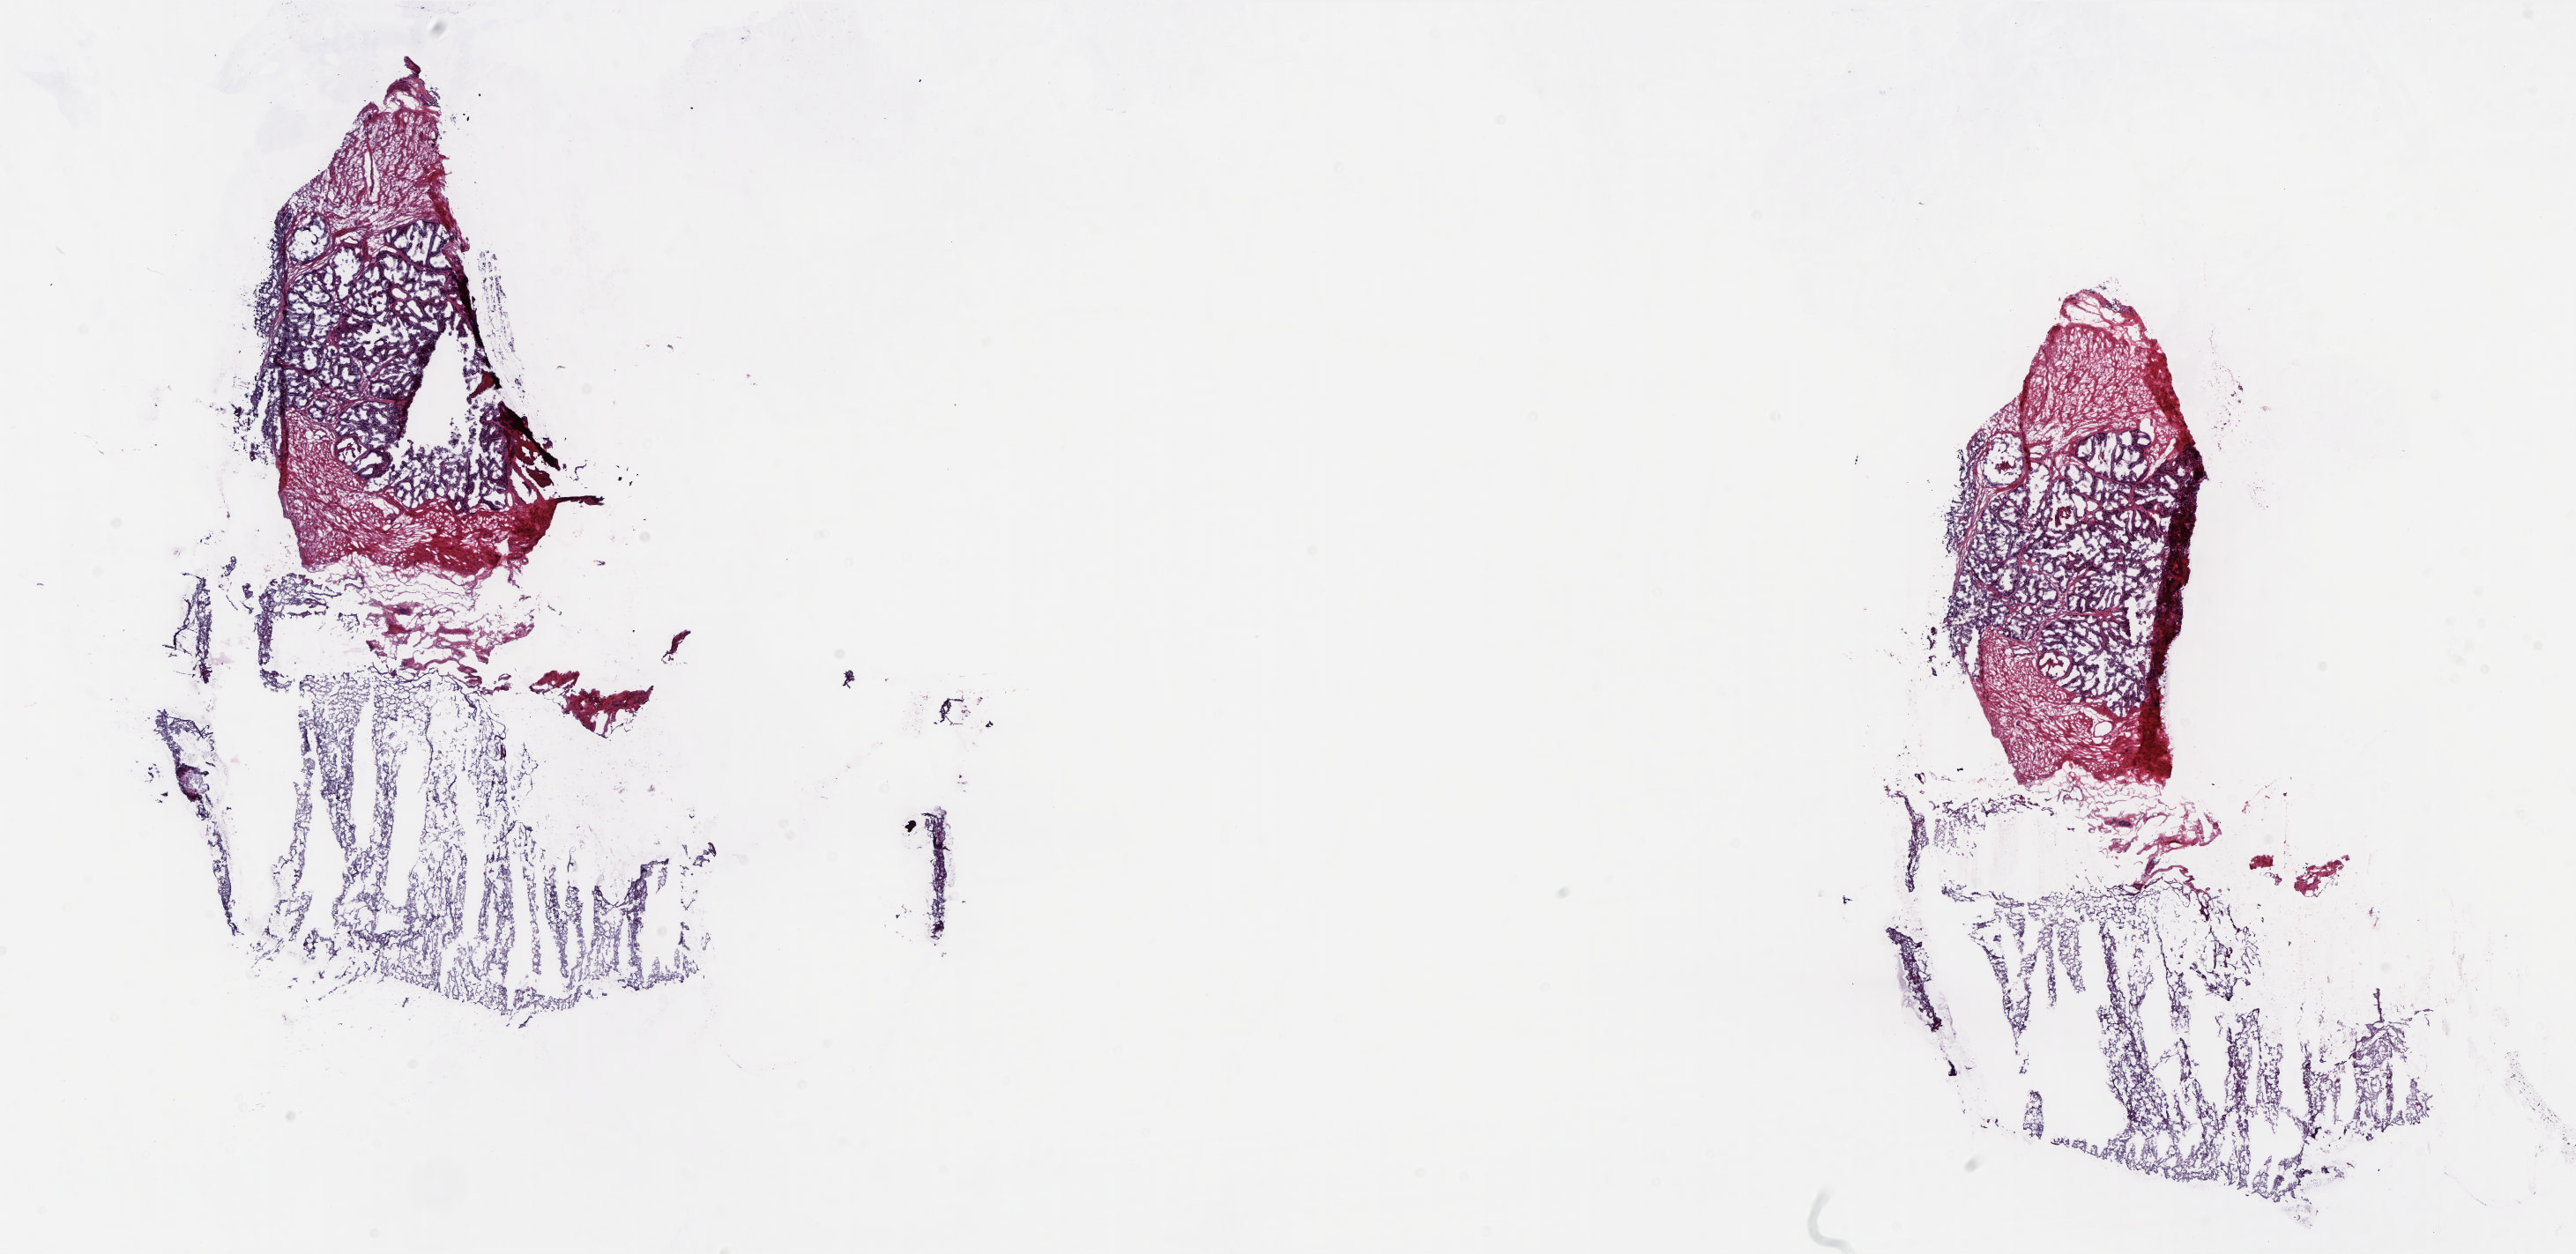
Digitized H&E tissue section (whole slide) — a low-resolution overview of the entire scanned area, about 23.6 x 11.5 mm (slide scanned at 20x). Frozen section from the top of the tissue portion. Prostate, solid tissue normal (non-tumour tissue) sample. Male, age 64 years at initial diagnosis. Slide review estimates, as recorded: tumour cells 0%, tumour nuclei 0%, normal cells 100%, stromal cells 0%, necrosis 0%. Inflammatory infiltration, as recorded: lymphocyte infiltration 3%, monocyte infiltration 0%, neutrophil infiltration 0%.
This section: solid tissue normal sample (biorepository sample class). Patient diagnosis: Adenocarcinoma, NOS (prostate gland).